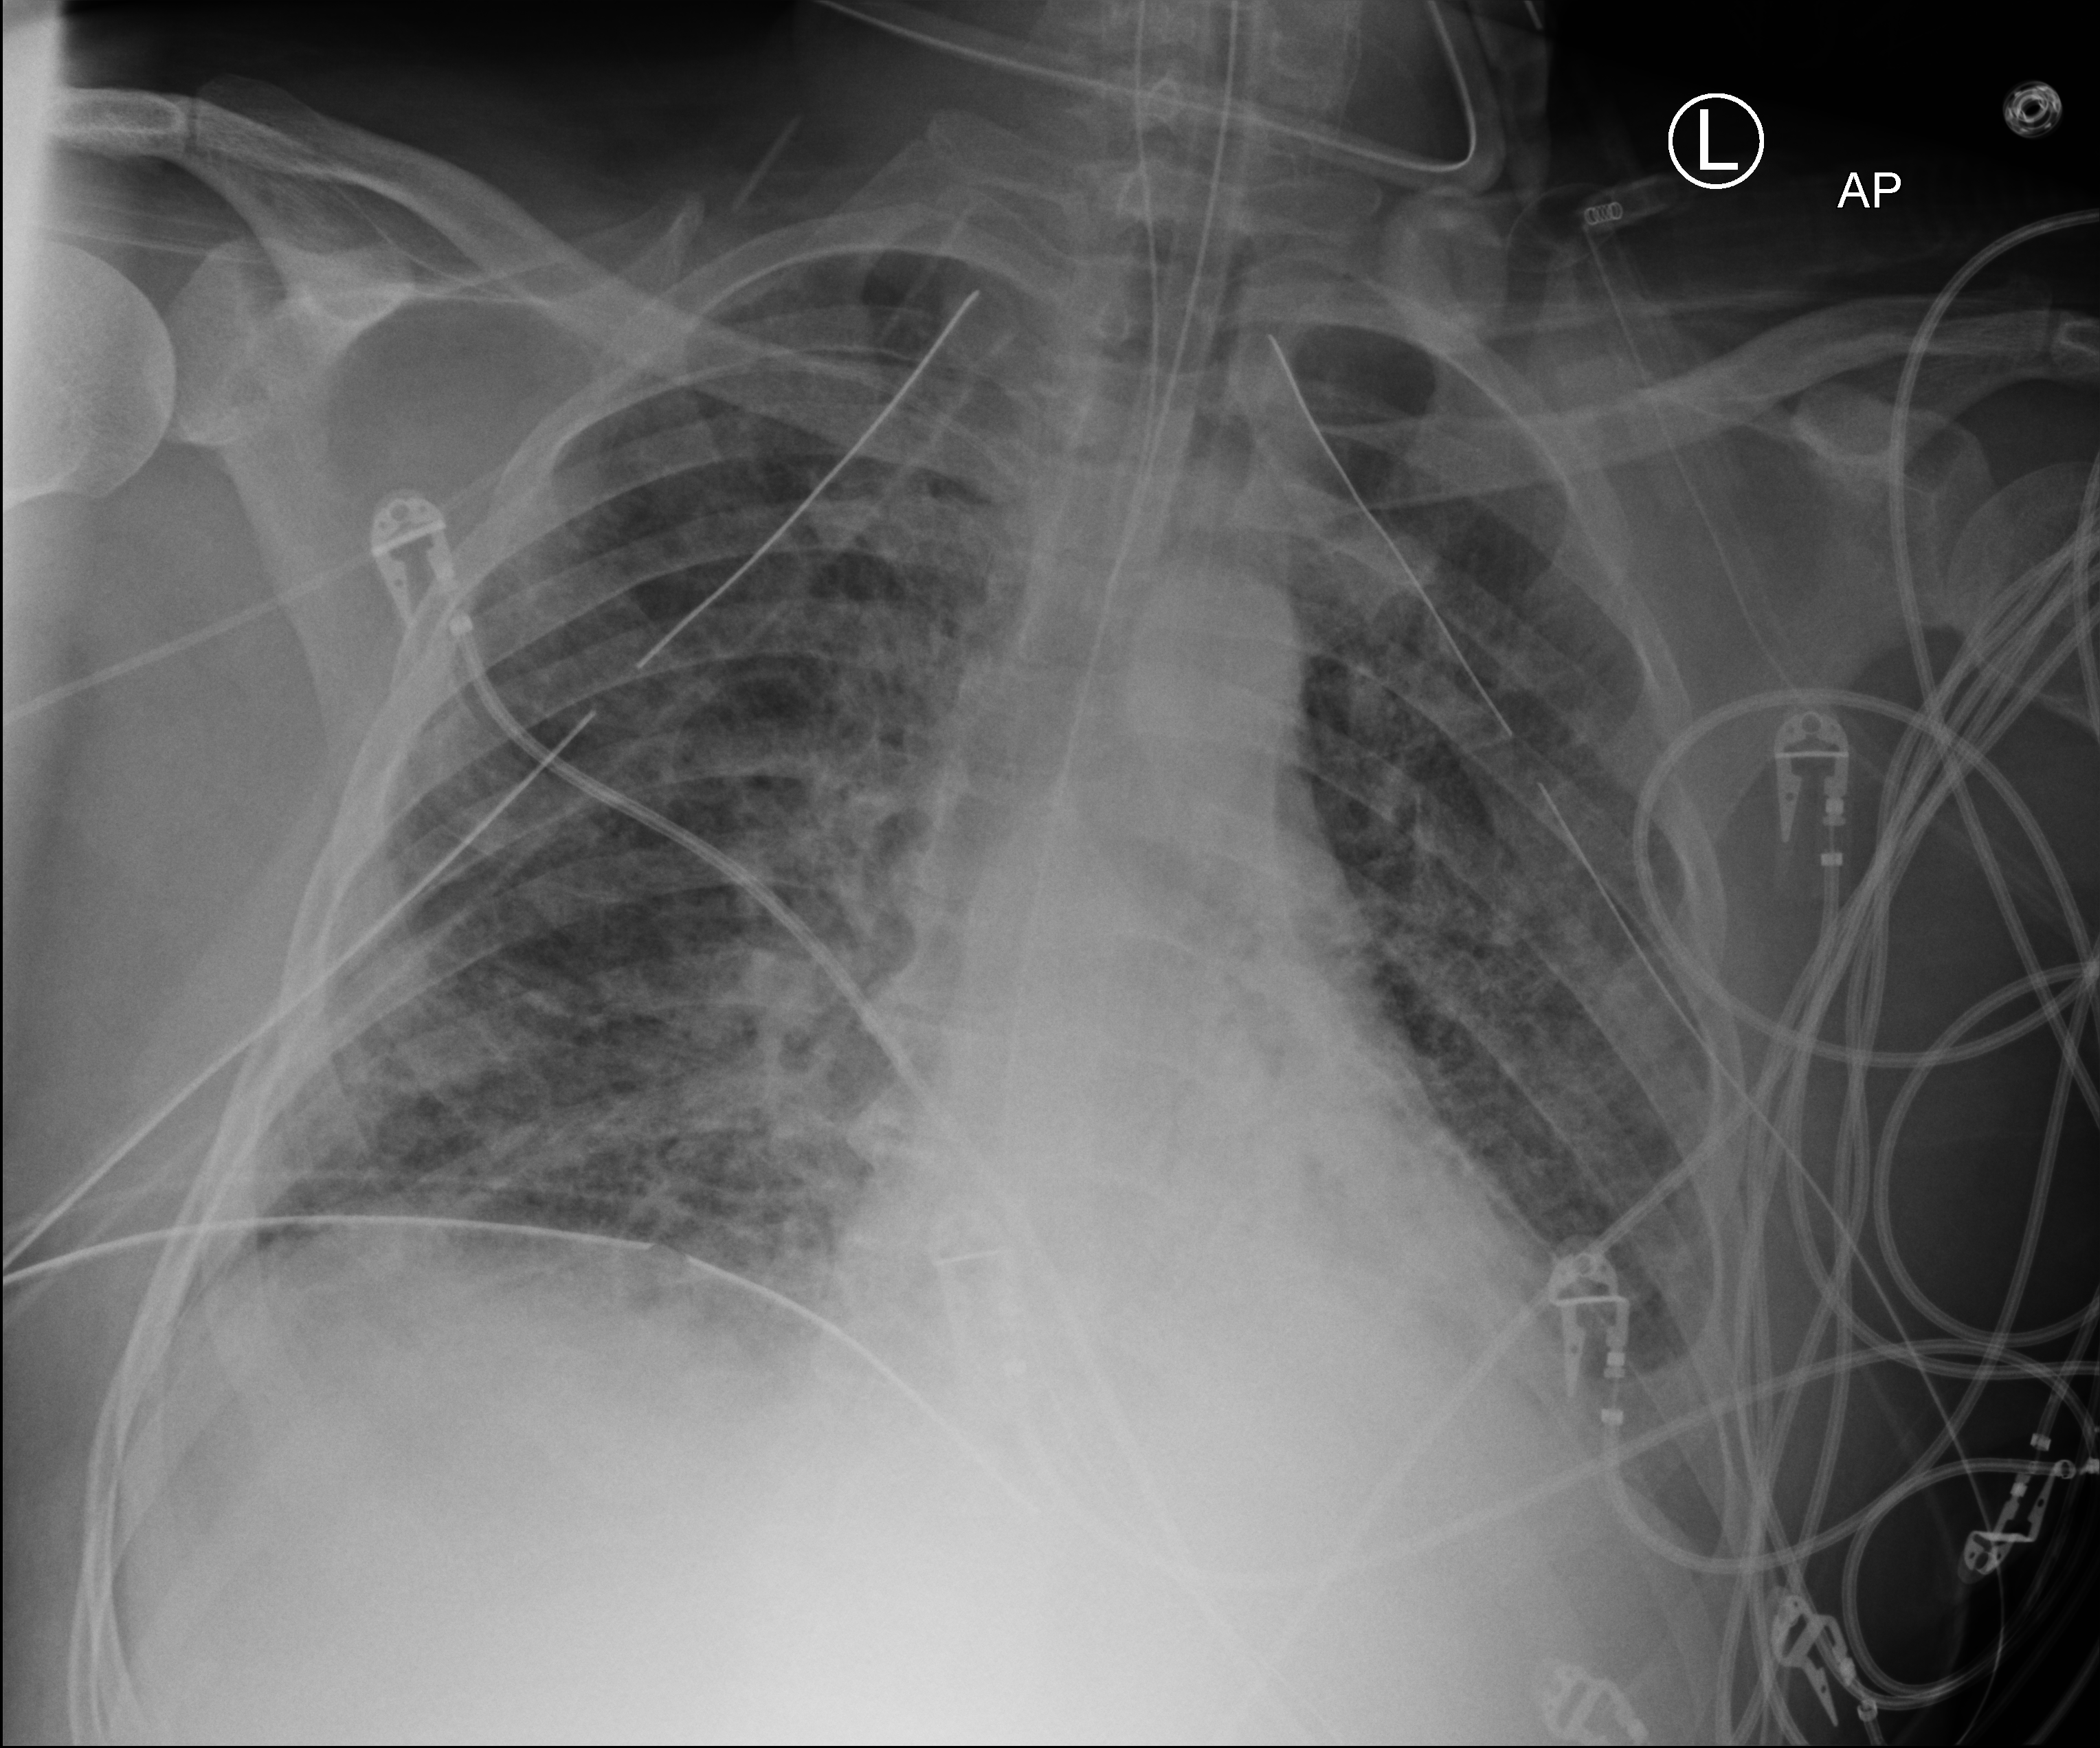
Portable chest radiograph; anteroposterior (AP) projection. Patient hospitalised with COVID-19; male, aged 18–59 years.
Admission-level facts for this patient (not findings on this image; timing relative to this image not recorded):
- admitted to intensive care during this hospital stay: yes
- chronic kidney disease (admission record): no